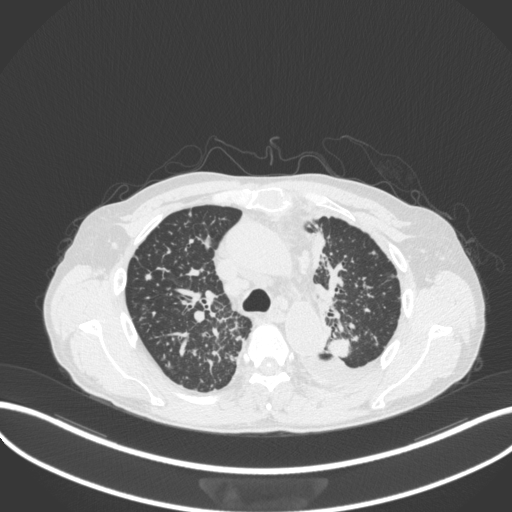
Chest CT, one axial slice; reconstruction kernel B31f; 120 kVp; lung window (W 1500 / L -600 HU); 1 mm slice thickness; 512 × 512 image matrix. Male patient, age 58 years. Case-level facts recorded for this patient, not image findings: clinical TNM (as recorded): T1c N3 M1.
Annotated regions visible in this slice (bounding box drawn by a radiologist):
- lung tumour (recorded histology: adenocarcinoma): bounding box (x1, y1, x2, y2) in pixels: (324, 332, 356, 364)